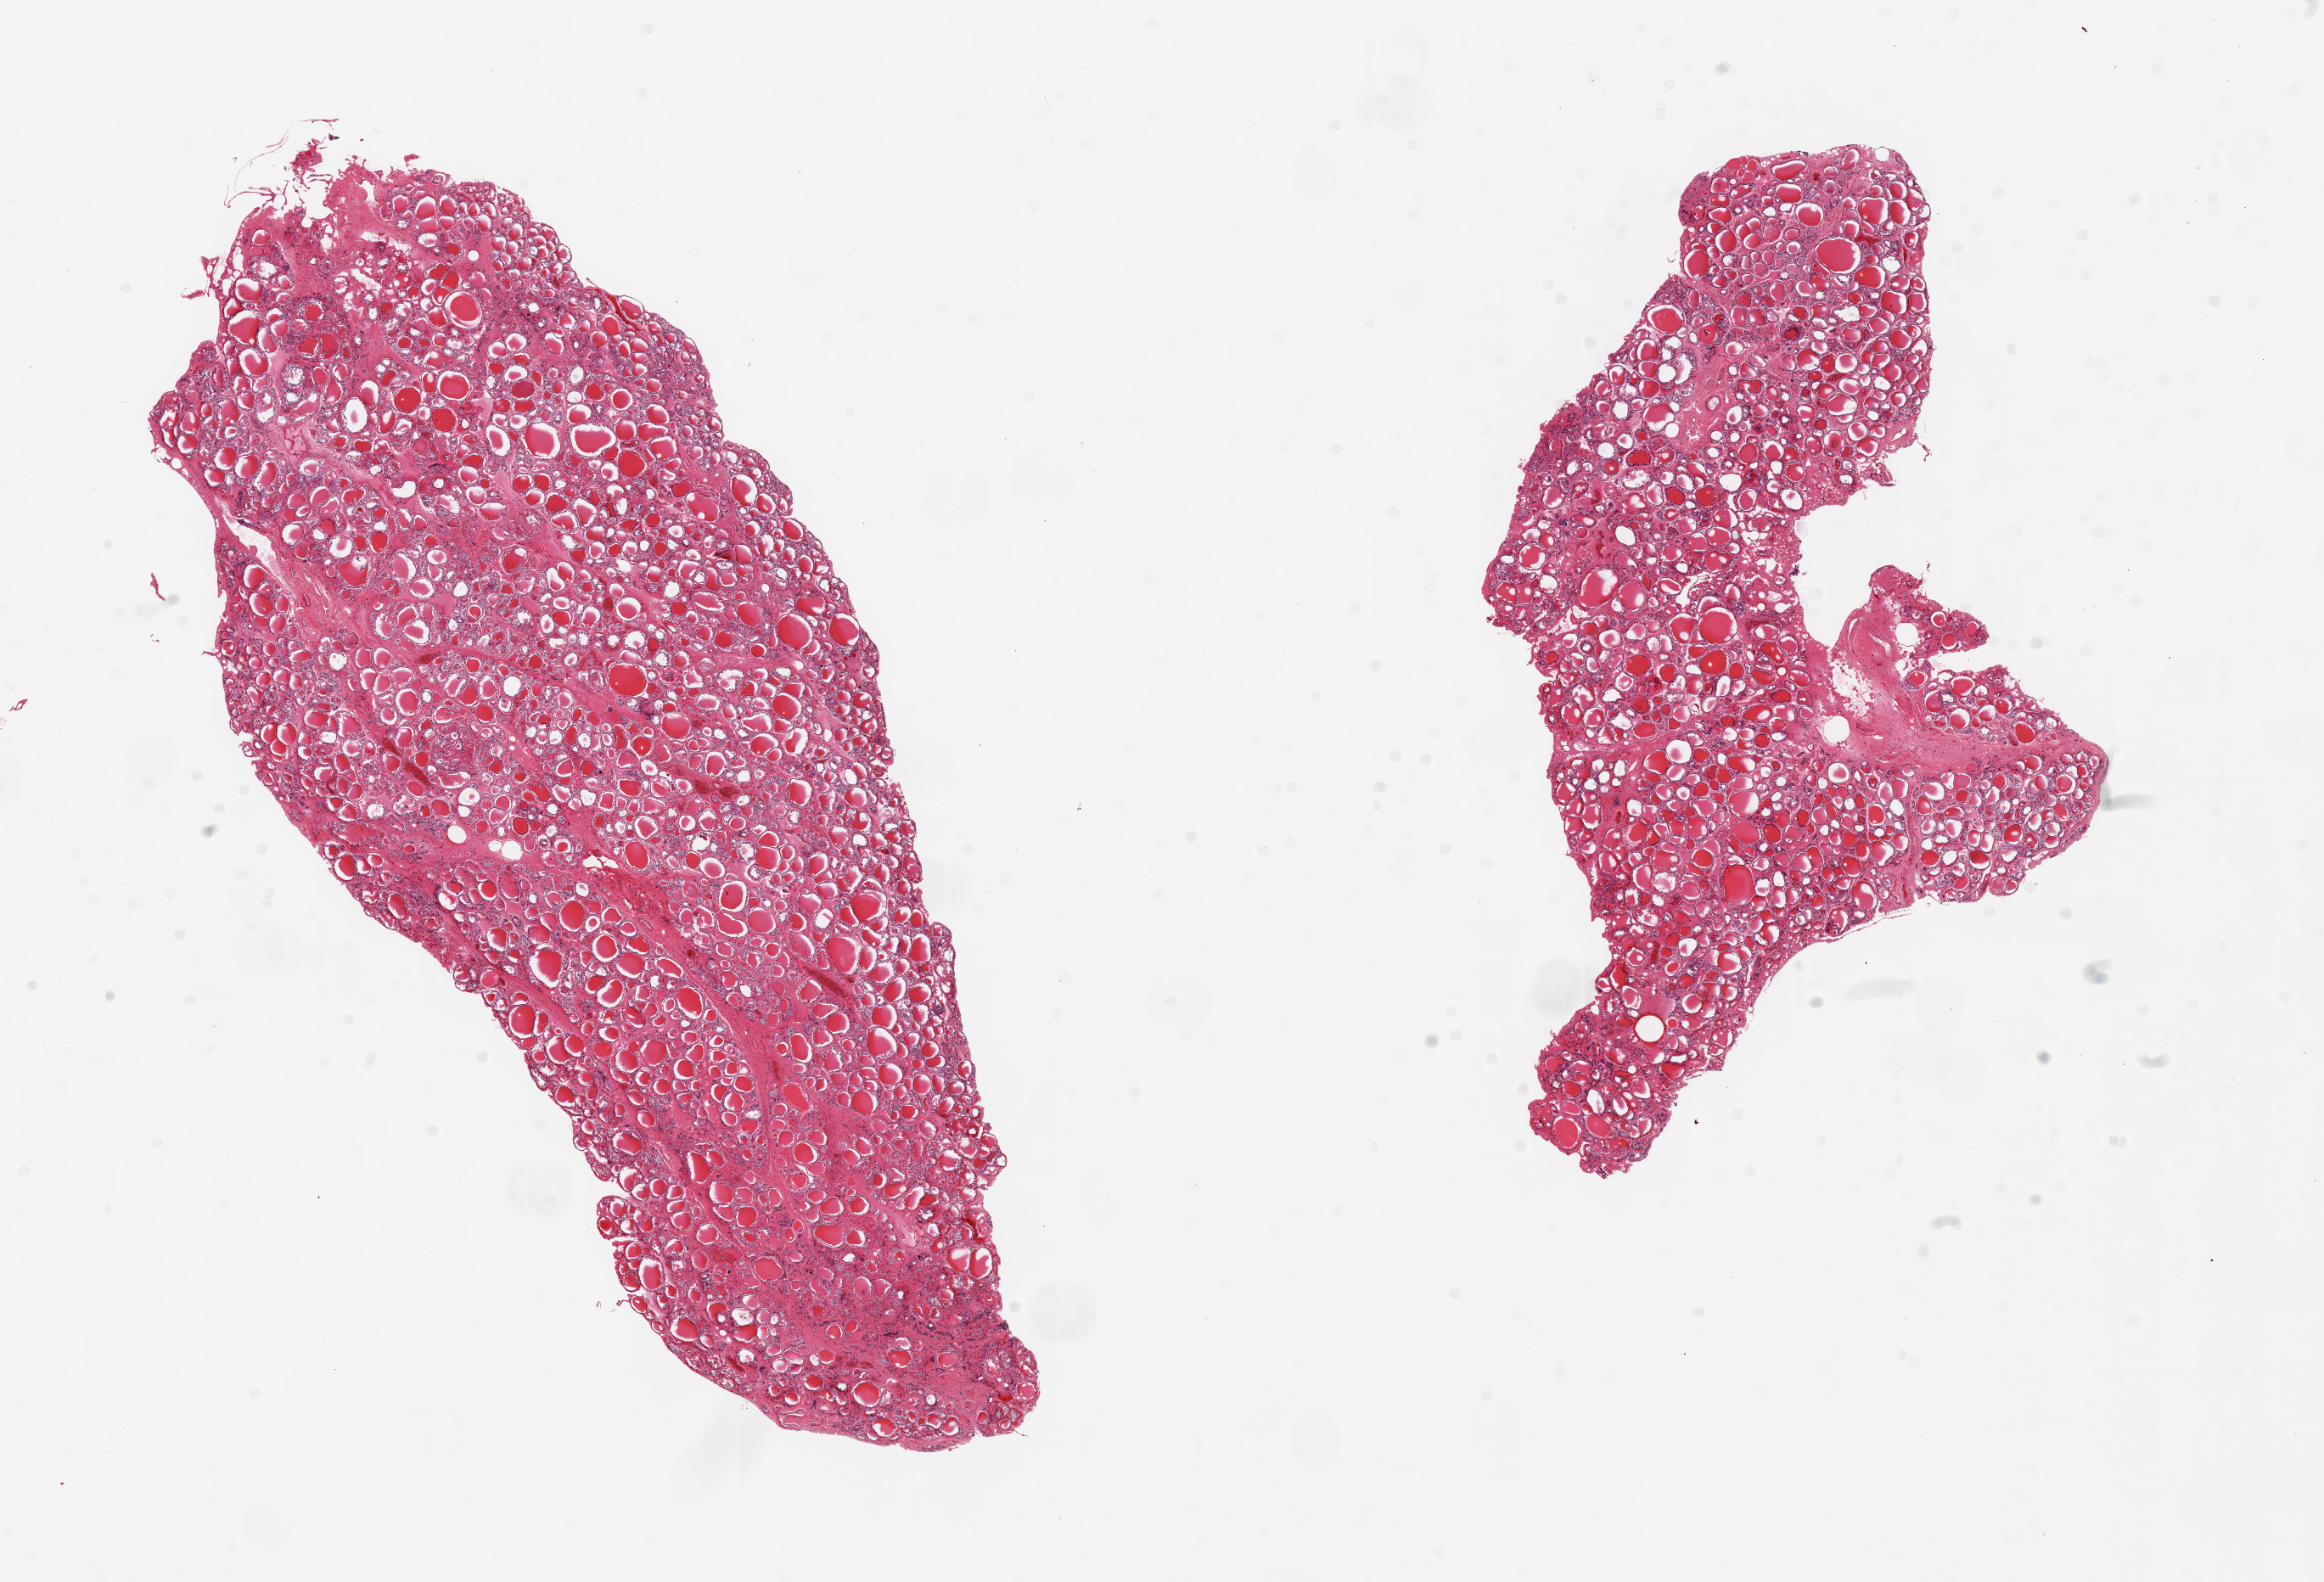
Digitized H&E-stained section, low-resolution overview of the scanned area, about 21.7 x 14.7 mm, PAXgene-fixed paraffin-embedded (PFPE) section, section of thyroid (target tissue), donor tissue sample. Female donor.
* review note (as recorded): 2 pieces; interstitial fibrosis with some nodularity